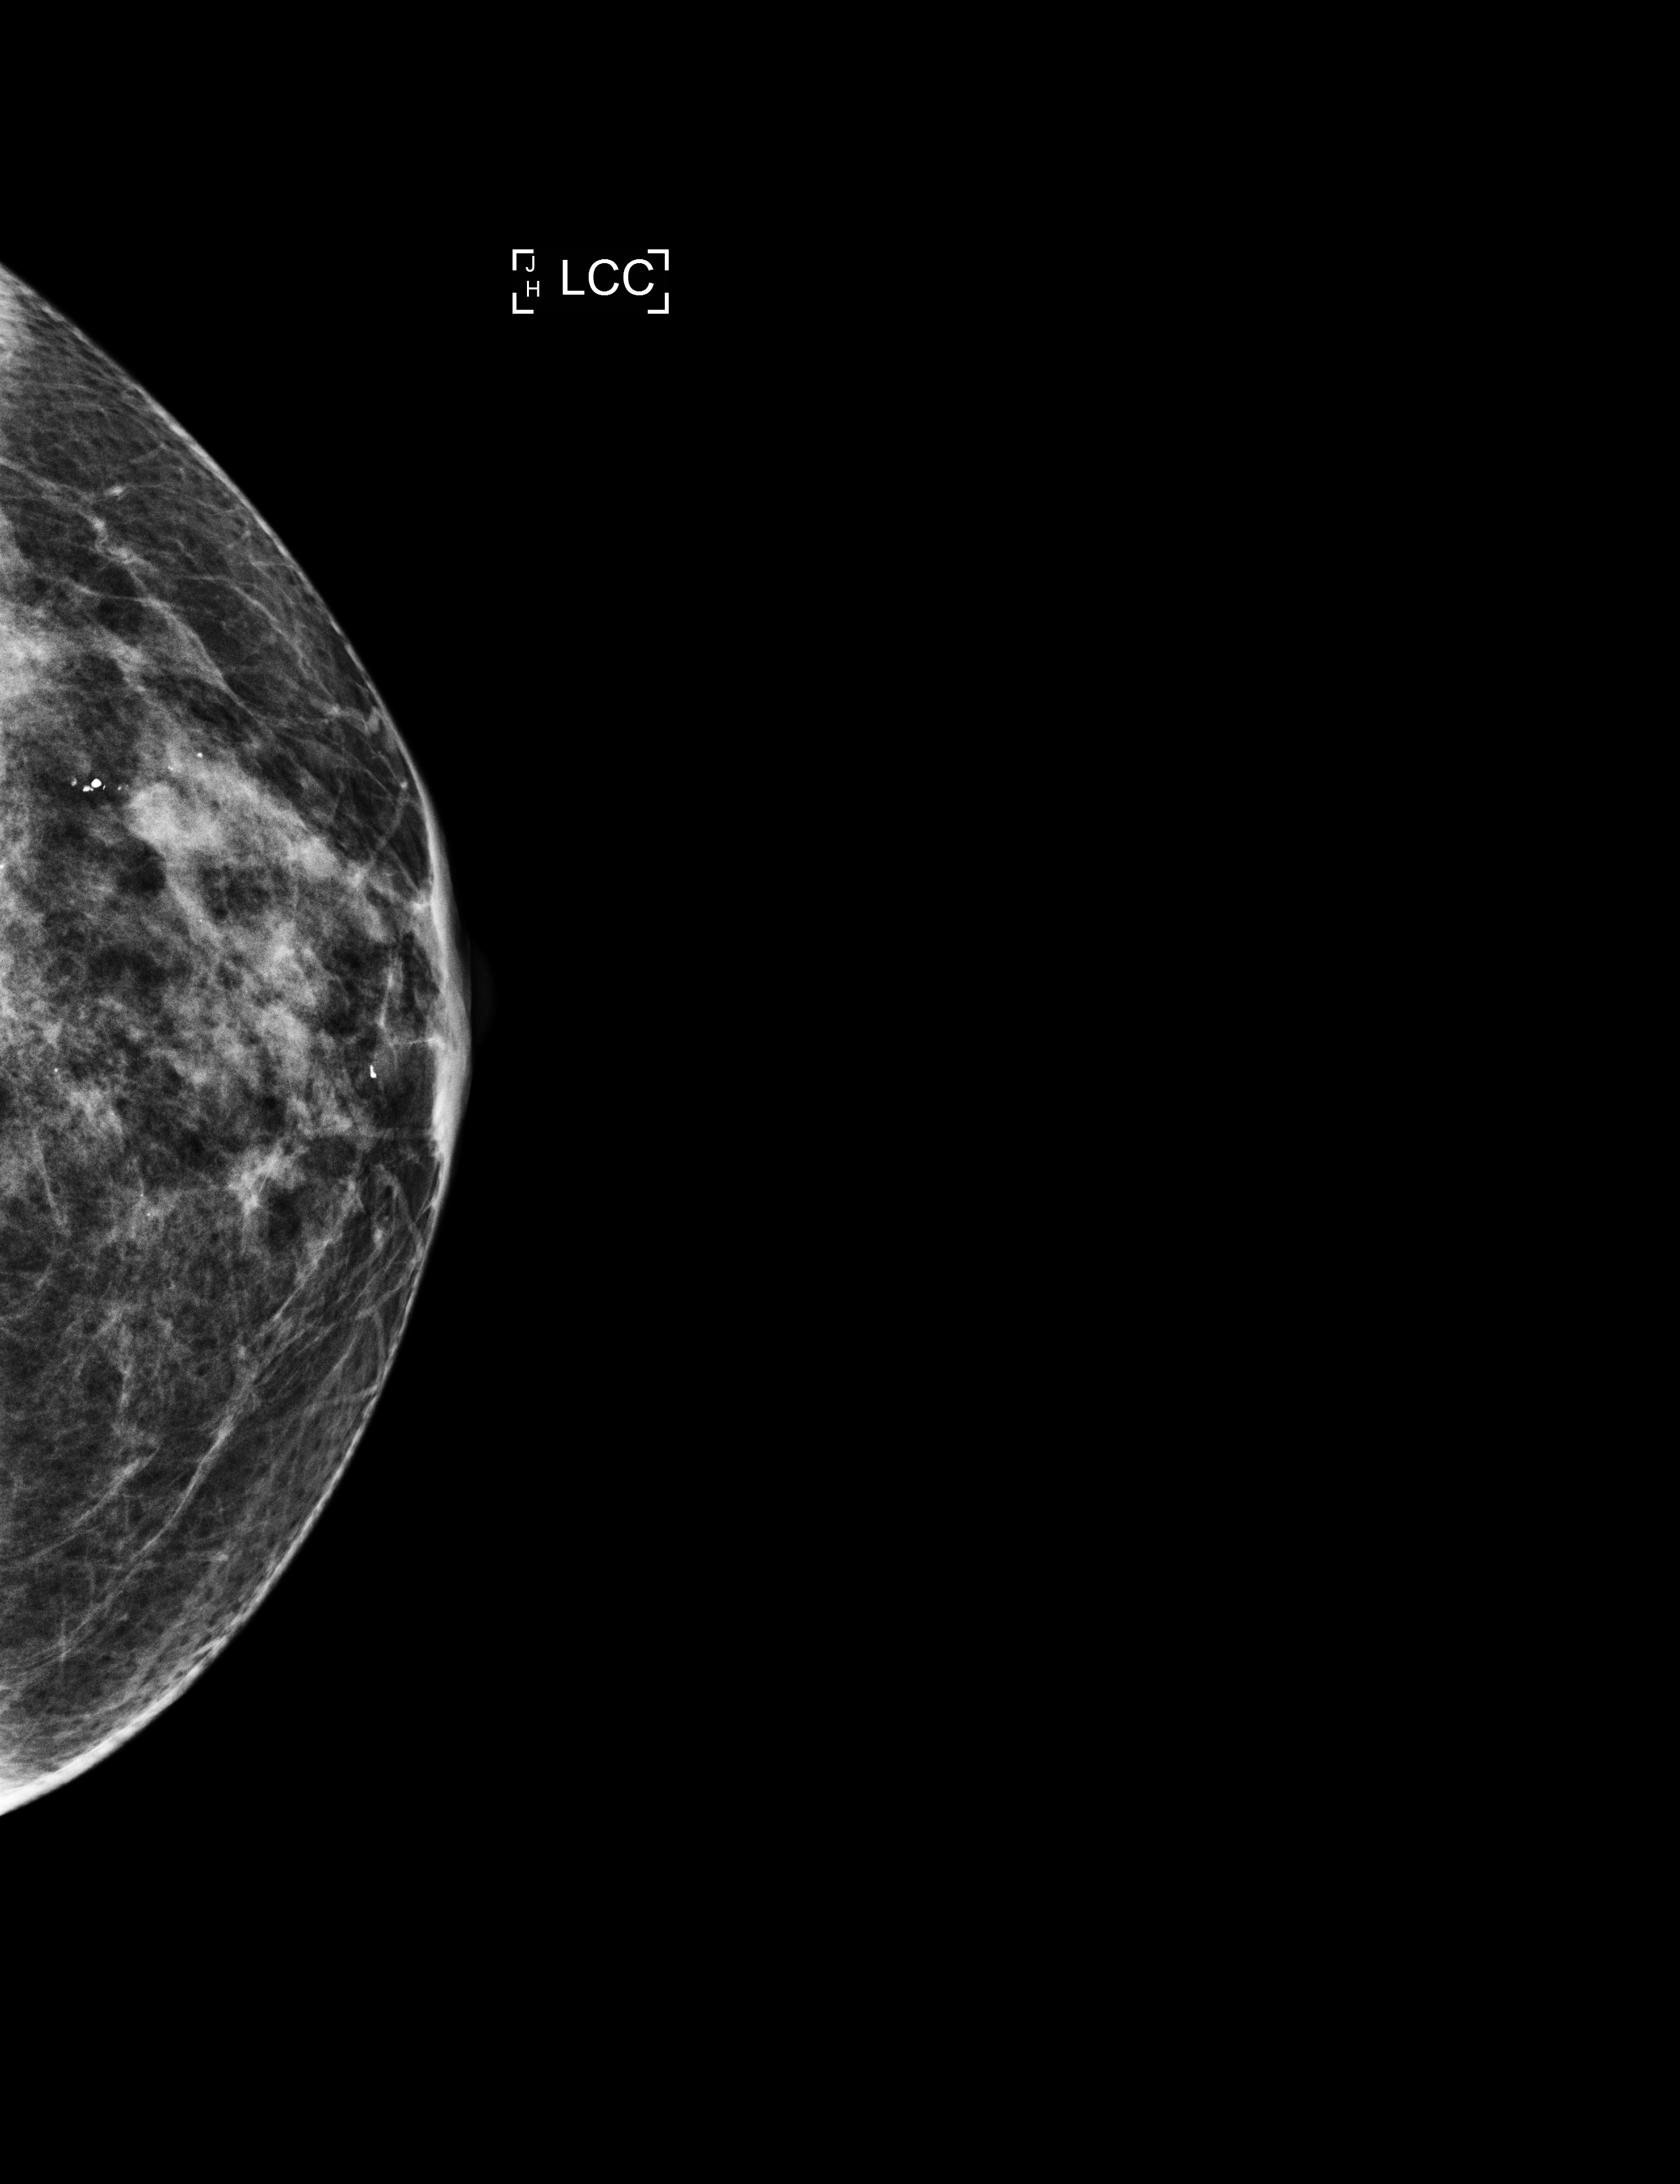
Digital mammogram (FFDM), left breast, cranio-caudal projection, screening examination, system: Selenia Dimensions. Patient: female, 74 years.
BI-RADS breast density category at the screening exam (both breasts, scale 1–4): 3. Final BI-RADS assessment for this screening round (tomosynthesis exam, both breasts): category 2. Recall: no recall after this screen.